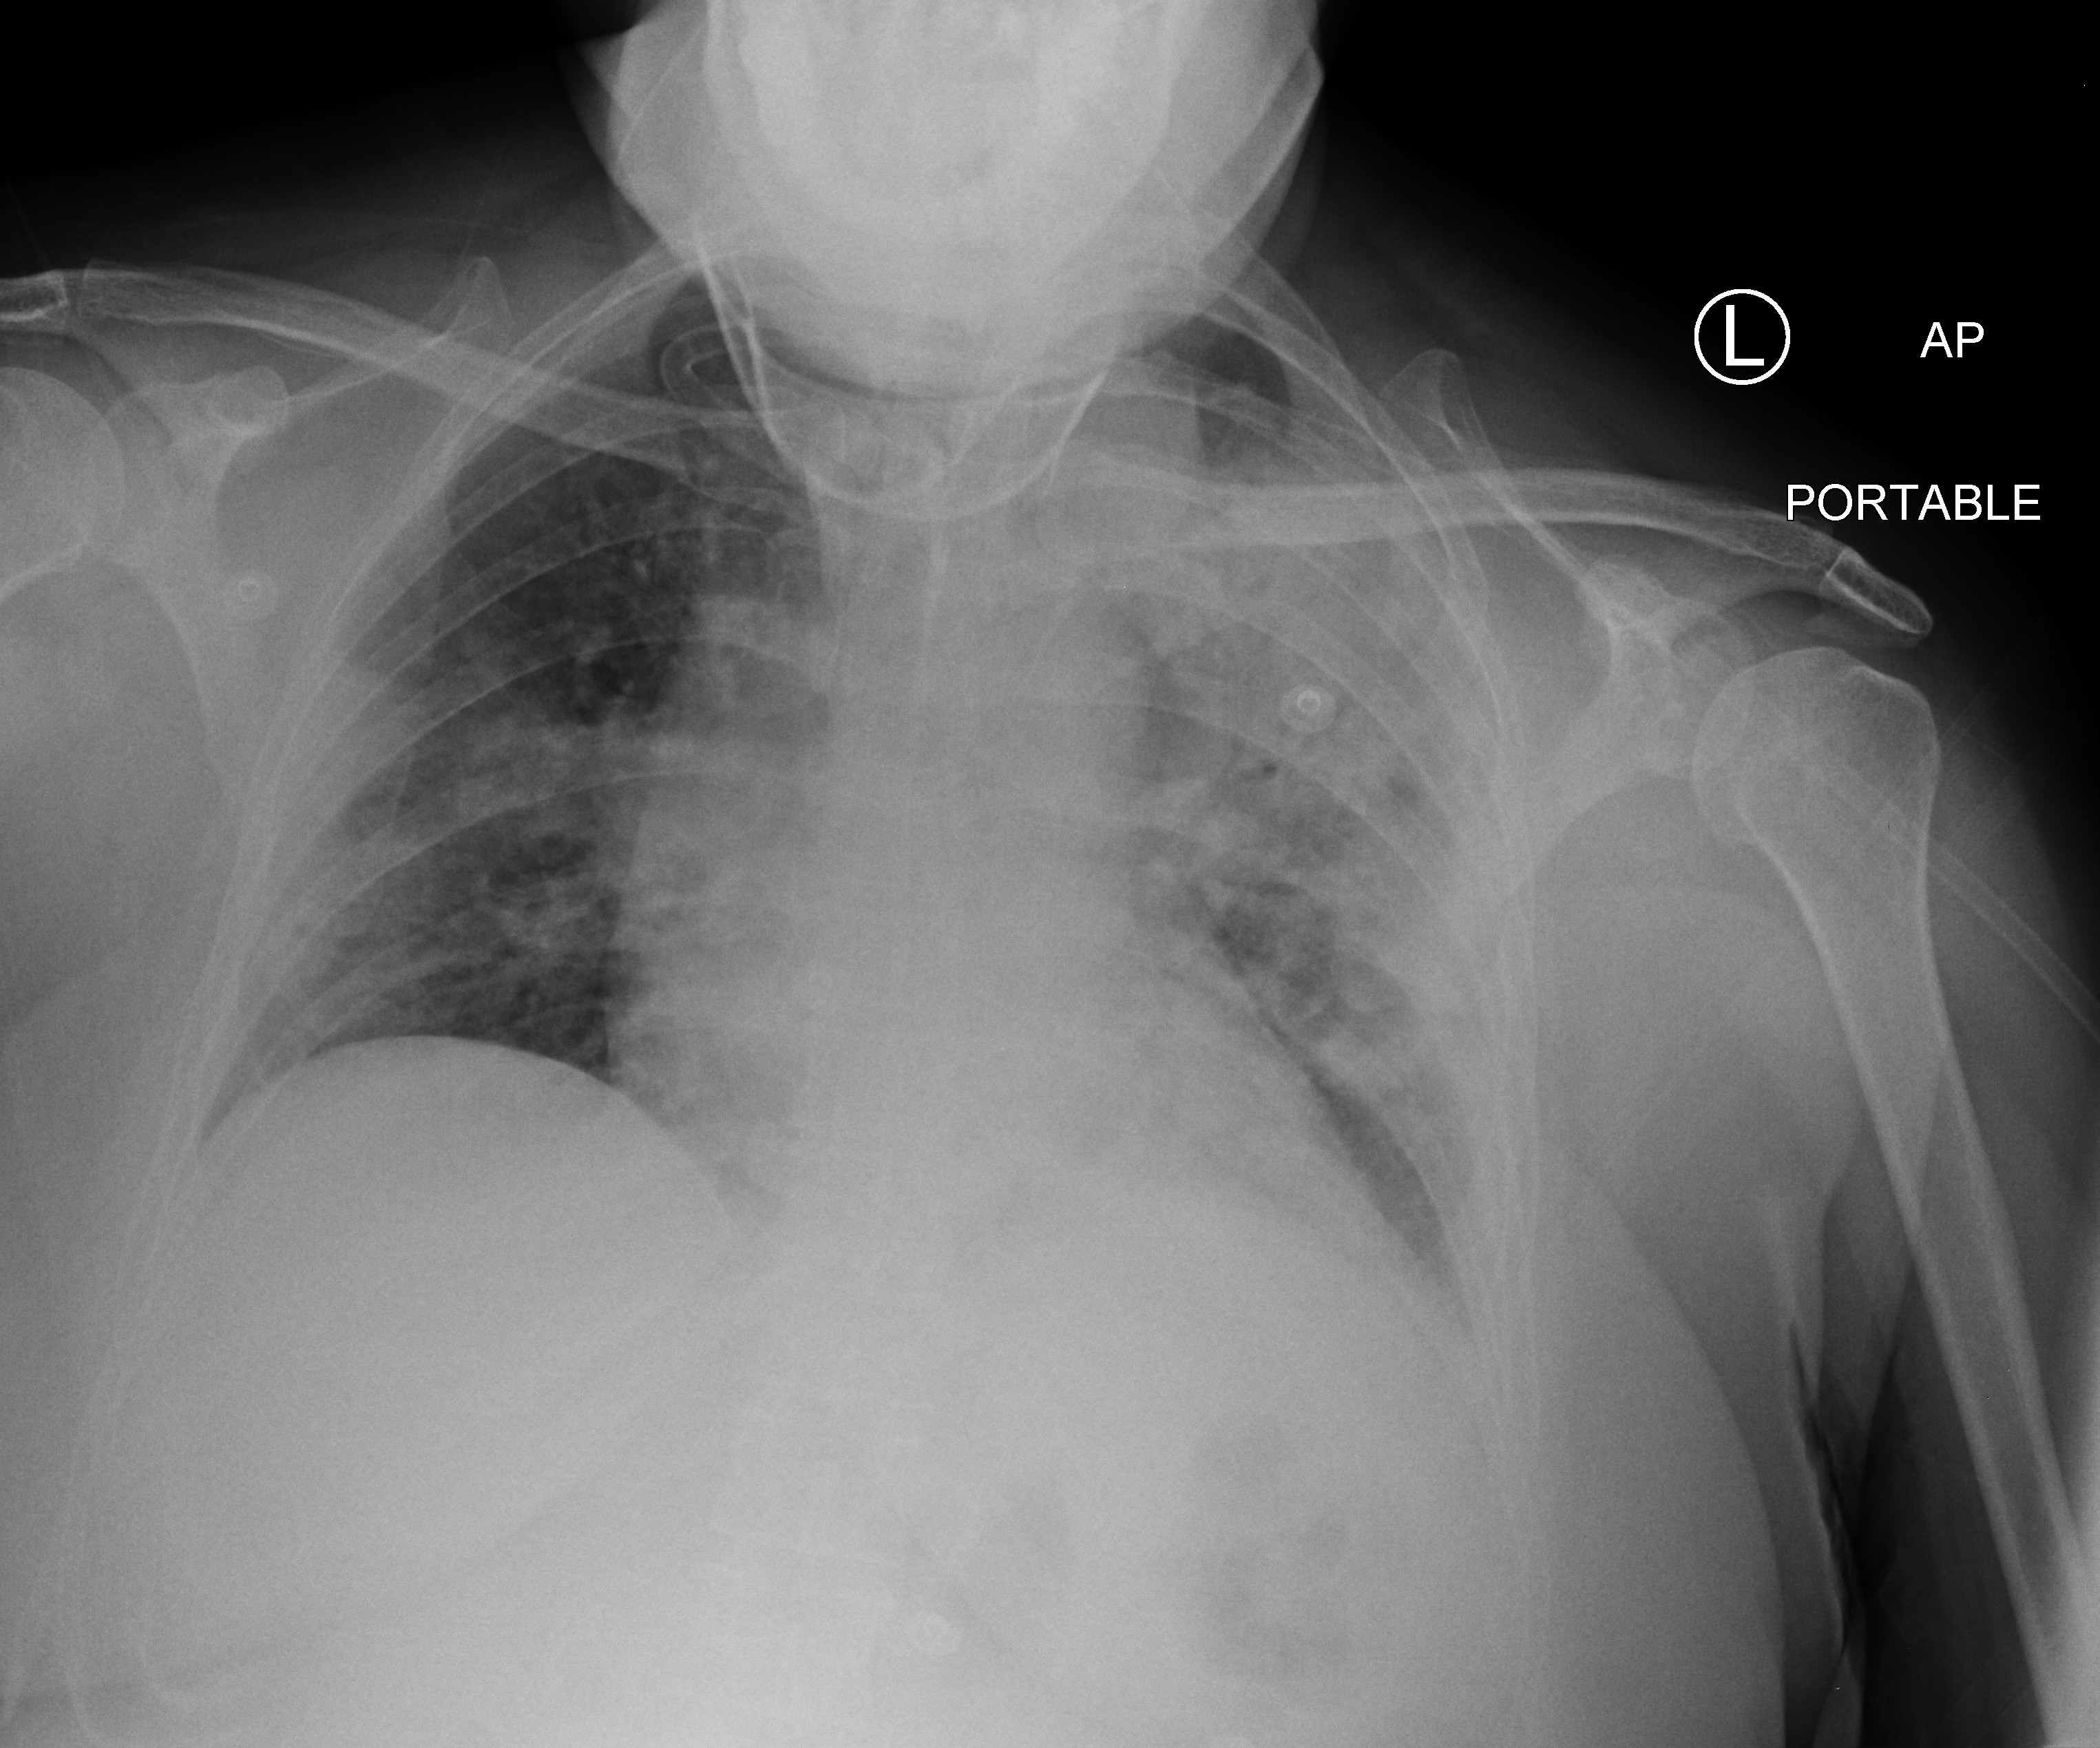
Bedside chest radiograph (computed radiography), anteroposterior (AP) projection. Female patient hospitalised with COVID-19, age 18–59 years.
Admission-level facts for this patient (not findings on this image; timing relative to this image not recorded):
- length of hospital stay: 22 days
- admitted to intensive care during this hospital stay: yes